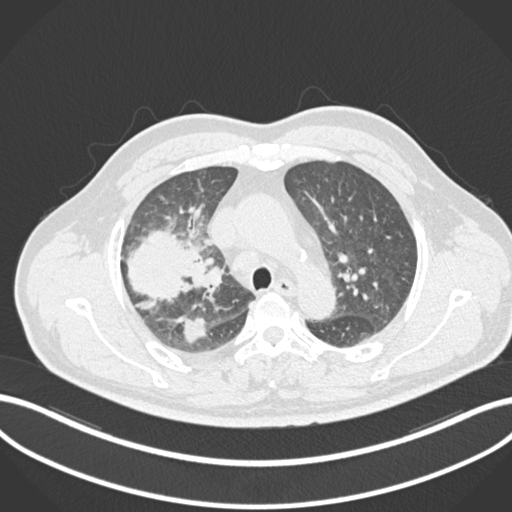
Chest CT, one axial slice. Slice 663 of 852 in the series (ordered by position). Reconstruction kernel B30f. 120 kVp. Lung window (W 1500 / L -600 HU). 512 × 512 image matrix, field of view 400 × 400 mm. Male patient, age 55 years. From the clinical record (not read from this slice): clinical TNM (as recorded): T3 N2 M1.
Outlined on this slice (bounding box drawn by a radiologist):
- lung tumour (recorded histology: adenocarcinoma): bounding box [x1, y1, x2, y2] px = [123, 224, 210, 302]